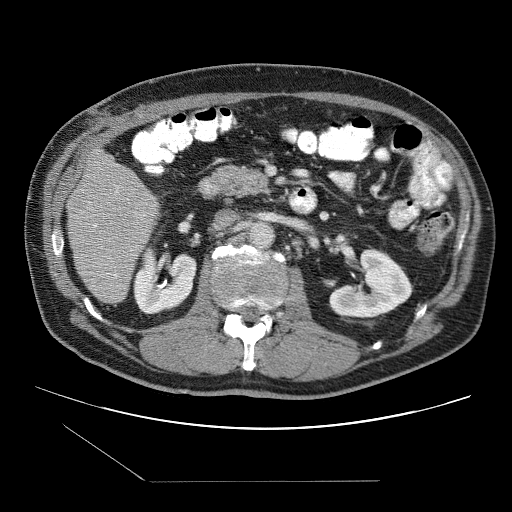
Contrast-enhanced abdominal CT (liver protocol), one axial slice. Position 33 of 109 along the scan axis. 120 kVp. One of 2 acquisitions stored at this slice position. Soft-tissue window (W 400 / L 40 HU). 512 × 512 image matrix. From the clinical record (not read from this slice): diagnosis: hepatocellular carcinoma (patient treated with transarterial chemoembolisation; whether this scan precedes or follows treatment is not stated here); TNM stage (as recorded): Stage-IIIB; Child-Pugh class: A.
Structures marked on this image (semi-automatic segmentation, software-assisted and operator-edited):
- liver parenchyma outside the tumour (the mass and vessels are separate outlines, so this box may not span the whole liver): bounding box [x1, y1, x2, y2] px = [66, 147, 160, 302]
- liver vessels: [93, 190, 117, 277]